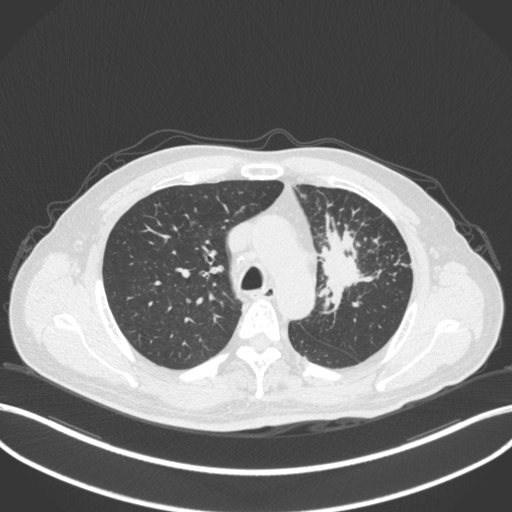
Chest CT, one axial slice; slice 250 of 386 in the series (ordered by position); reconstruction kernel B31f; 120 kVp; lung window (W 1500 / L -600 HU); 1 mm slice thickness; 512 × 512 image matrix. Male patient, age 69 years. Case-level facts recorded for this patient, not image findings: clinical TNM (as recorded): T2a N2 M0; histopathological grade: G2-3.
Outlined on this slice (bounding box drawn by a radiologist):
- lung tumour (recorded histology: adenocarcinoma): bounding box (x1, y1, x2, y2) in pixels: (317, 216, 390, 320)